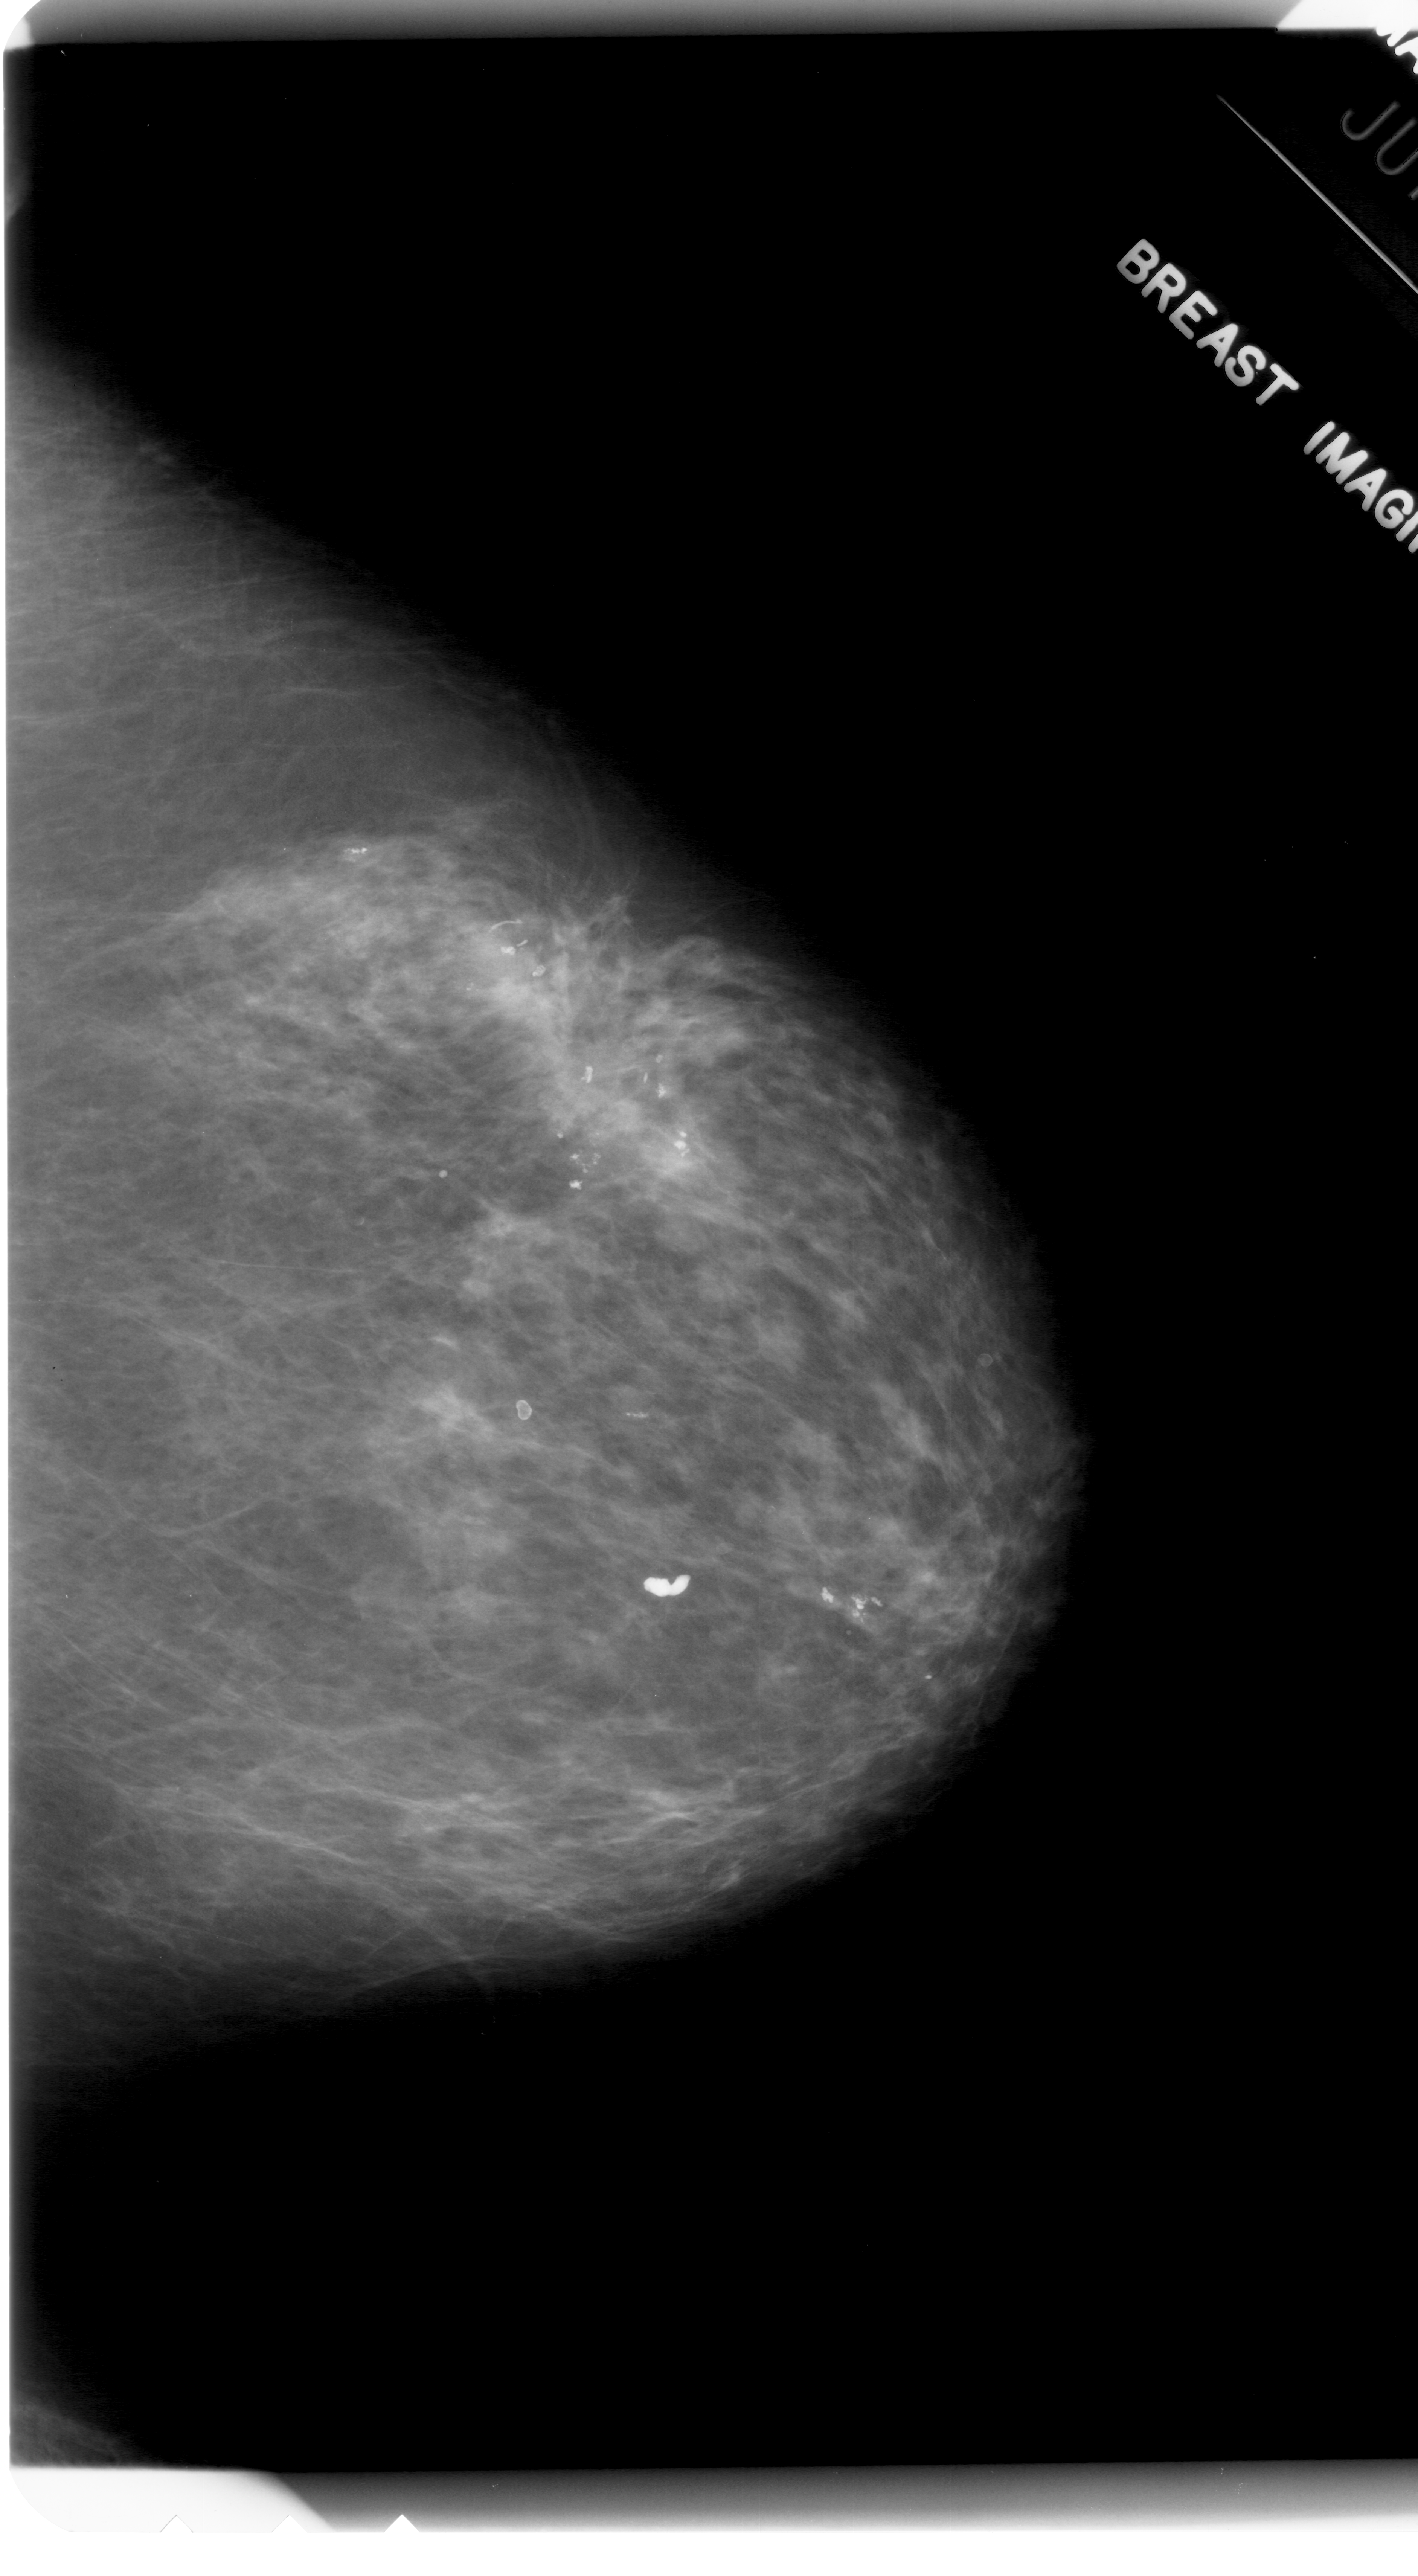
Scanned film-screen mammogram; right breast; craniocaudal (CC) view; 1418 × 2576 image matrix.
Expert-marked regions of interest on this image (one box per marked abnormality):
- Finding 1 of 3: calcifications, morphology dystrophic, distribution clustered; BI-RADS assessment category 3; pathology (as recorded): benign: bounding box (x1, y1, x2, y2) in pixels: (329, 836, 391, 874)
- Finding 2 of 3: calcifications, morphology dystrophic, distribution clustered; BI-RADS assessment category 3; subtlety rating 4 on a 1 (subtle) to 5 (obvious) scale; pathology (as recorded): benign: (561, 1116, 620, 1193)
- Finding 3 of 3: calcifications, morphology dystrophic, distribution clustered; BI-RADS assessment category 3; subtlety rating 4 on a 1 (subtle) to 5 (obvious) scale; pathology result (as recorded, not read from the image): benign: (805, 1568, 906, 1630)